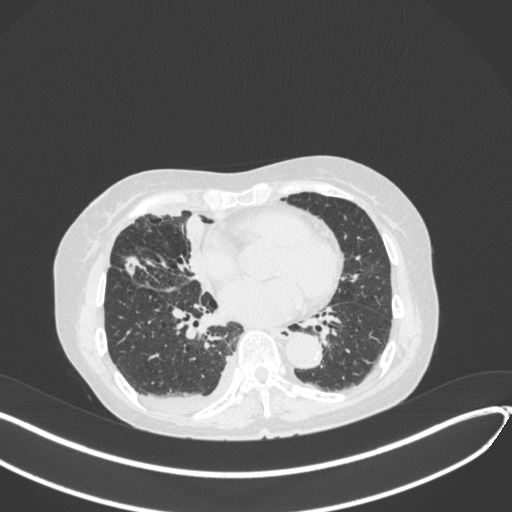
Chest CT, one axial slice. Position 167 of 418 along the scan axis. Reconstruction kernel B31f. Lung window (W 1500 / L -600 HU). 1 mm slice thickness. 512 × 512 image matrix. Patient: female, 75 years. Case-level facts recorded for this patient, not image findings: clinical TNM (as recorded): T2a N3 M0.
Annotated regions visible in this slice (bounding box drawn by a radiologist):
- lung tumour (recorded histology: adenocarcinoma): box from (x=115, y=249) to (x=145, y=278) px